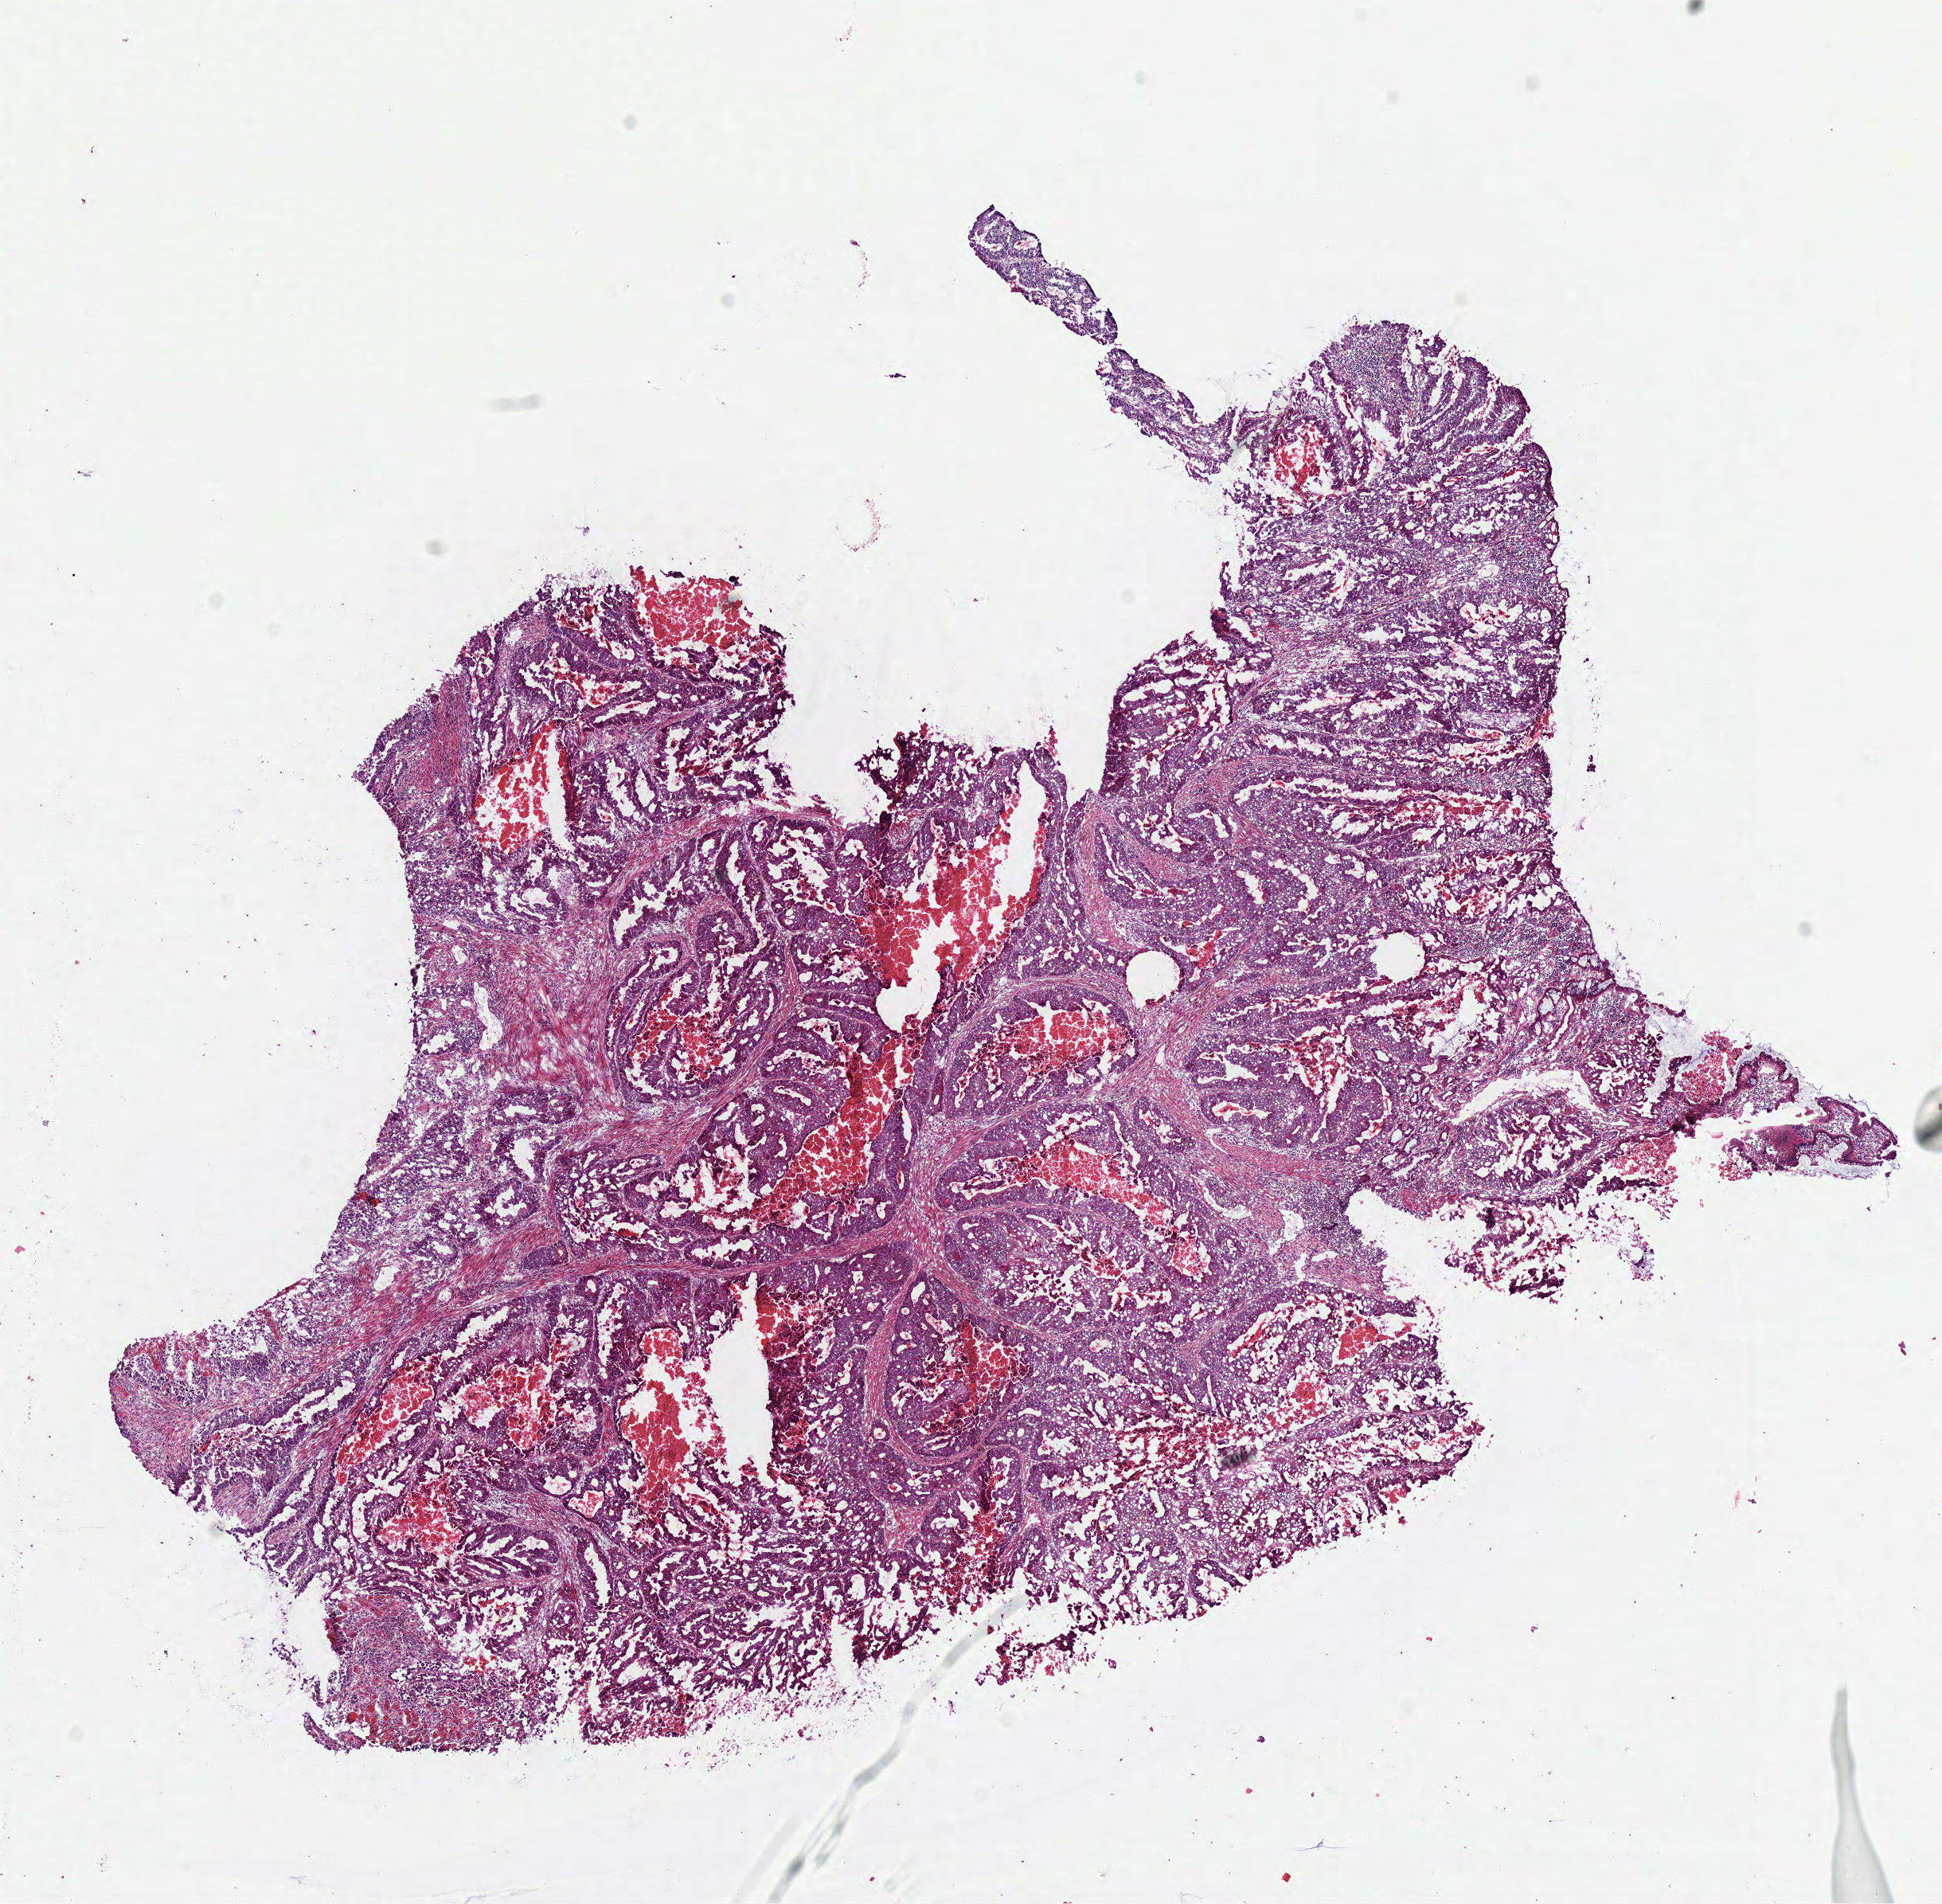
Digitized H&E-stained tissue section (whole slide), a low-resolution overview of the entire scanned area, about 9.6 x 9.4 mm, frozen section, colon, primary tumour sample. Patient: male, age at initial diagnosis 73 years. Pathologist review of this section (percent, as recorded): tumour cells 70%, tumour nuclei 70%, normal cells 0%, stromal cells 10%, necrosis 20%. Inflammatory infiltration, as recorded: lymphocyte infiltration 20%.
Diagnosis: Adenocarcinoma, NOS (ascending colon). AJCC pathologic stage: IIIB (7th edition).